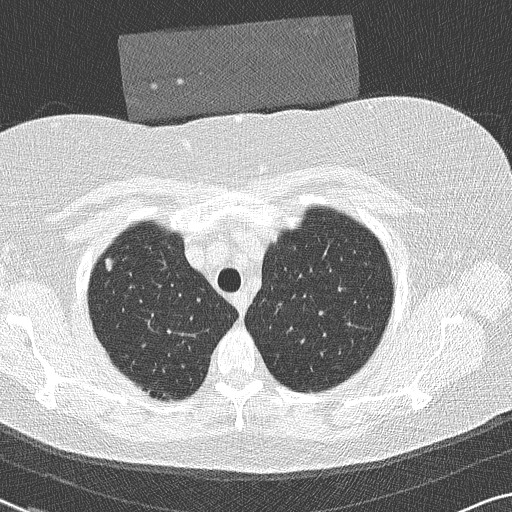
Axial slice from a low-dose chest CT screening exam, baseline annual screen, lung window (W 1500 / L -600 HU), 2 mm slice thickness, lung (sharp) reconstruction kernel (B50f), 120 kVp, slice 42 of 306 in the series. Female participant, aged 58 years at enrolment.
Expert reader's lesion annotation, bounding box (x1, y1, x2, y2) in pixels: (90, 245, 131, 291). No non-calcified nodule or mass ≥4 mm was recorded by the screening reader at this exam. Official screen result: negative screen, minor abnormalities not suspicious for lung cancer. Later outcome: lung cancer diagnosed 846 days after this screen — bronchiolo-alveolar adenocarcinoma, NOS, right upper lobe, well differentiated (G1), stage IA (AJCC 6th edition), 9 mm at pathology.